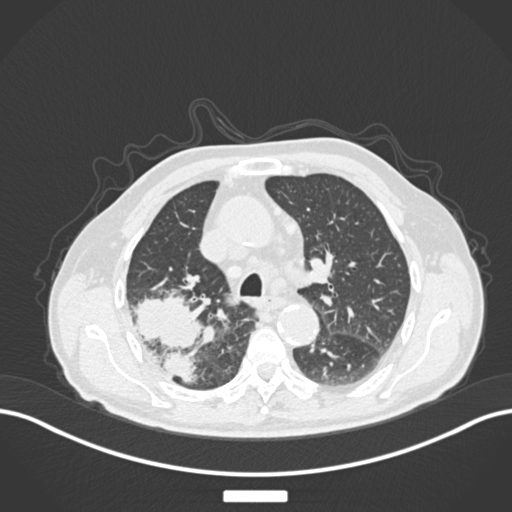
Chest CT, one axial slice. Position 125 of 201 along the scan axis. Lung window (W 1500 / L -600 HU). 1 mm slice thickness. 512 × 512 image matrix, field of view 400 × 400 mm. Patient: male, 72 years. Case-level facts recorded for this patient, not image findings: clinical TNM (as recorded): T3 N2 M0.
Structures marked on this image (rectangle marked by the reading radiologist):
- lung tumour (recorded histology: adenocarcinoma): bounding box [x1, y1, x2, y2] px = [131, 287, 203, 385]